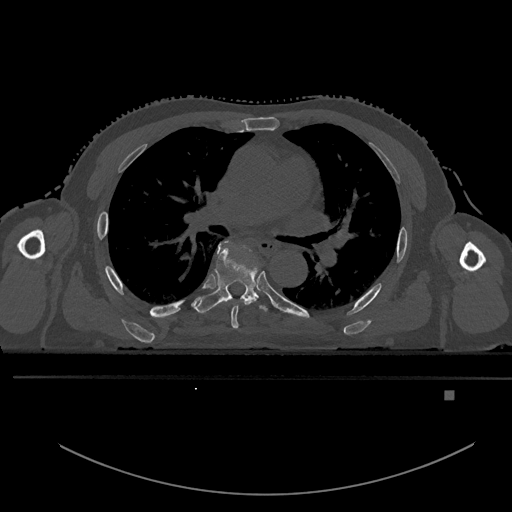
CT including the spine, one axial slice. Position 327 of 969 along the scan axis. Bone window (W 1800 / L 400 HU). 0.5 mm slice thickness. 512 × 512 image matrix. Patient: male, 82 years. Case-level facts recorded for this patient, not image findings: primary cancer: prostate.
Annotated regions visible in this slice (semi-automatic segmentation, software-assisted and operator-edited):
- T5 vertebra: bounding box [x1, y1, x2, y2] px = [224, 241, 256, 329]
- T6 vertebra: [191, 242, 268, 314]